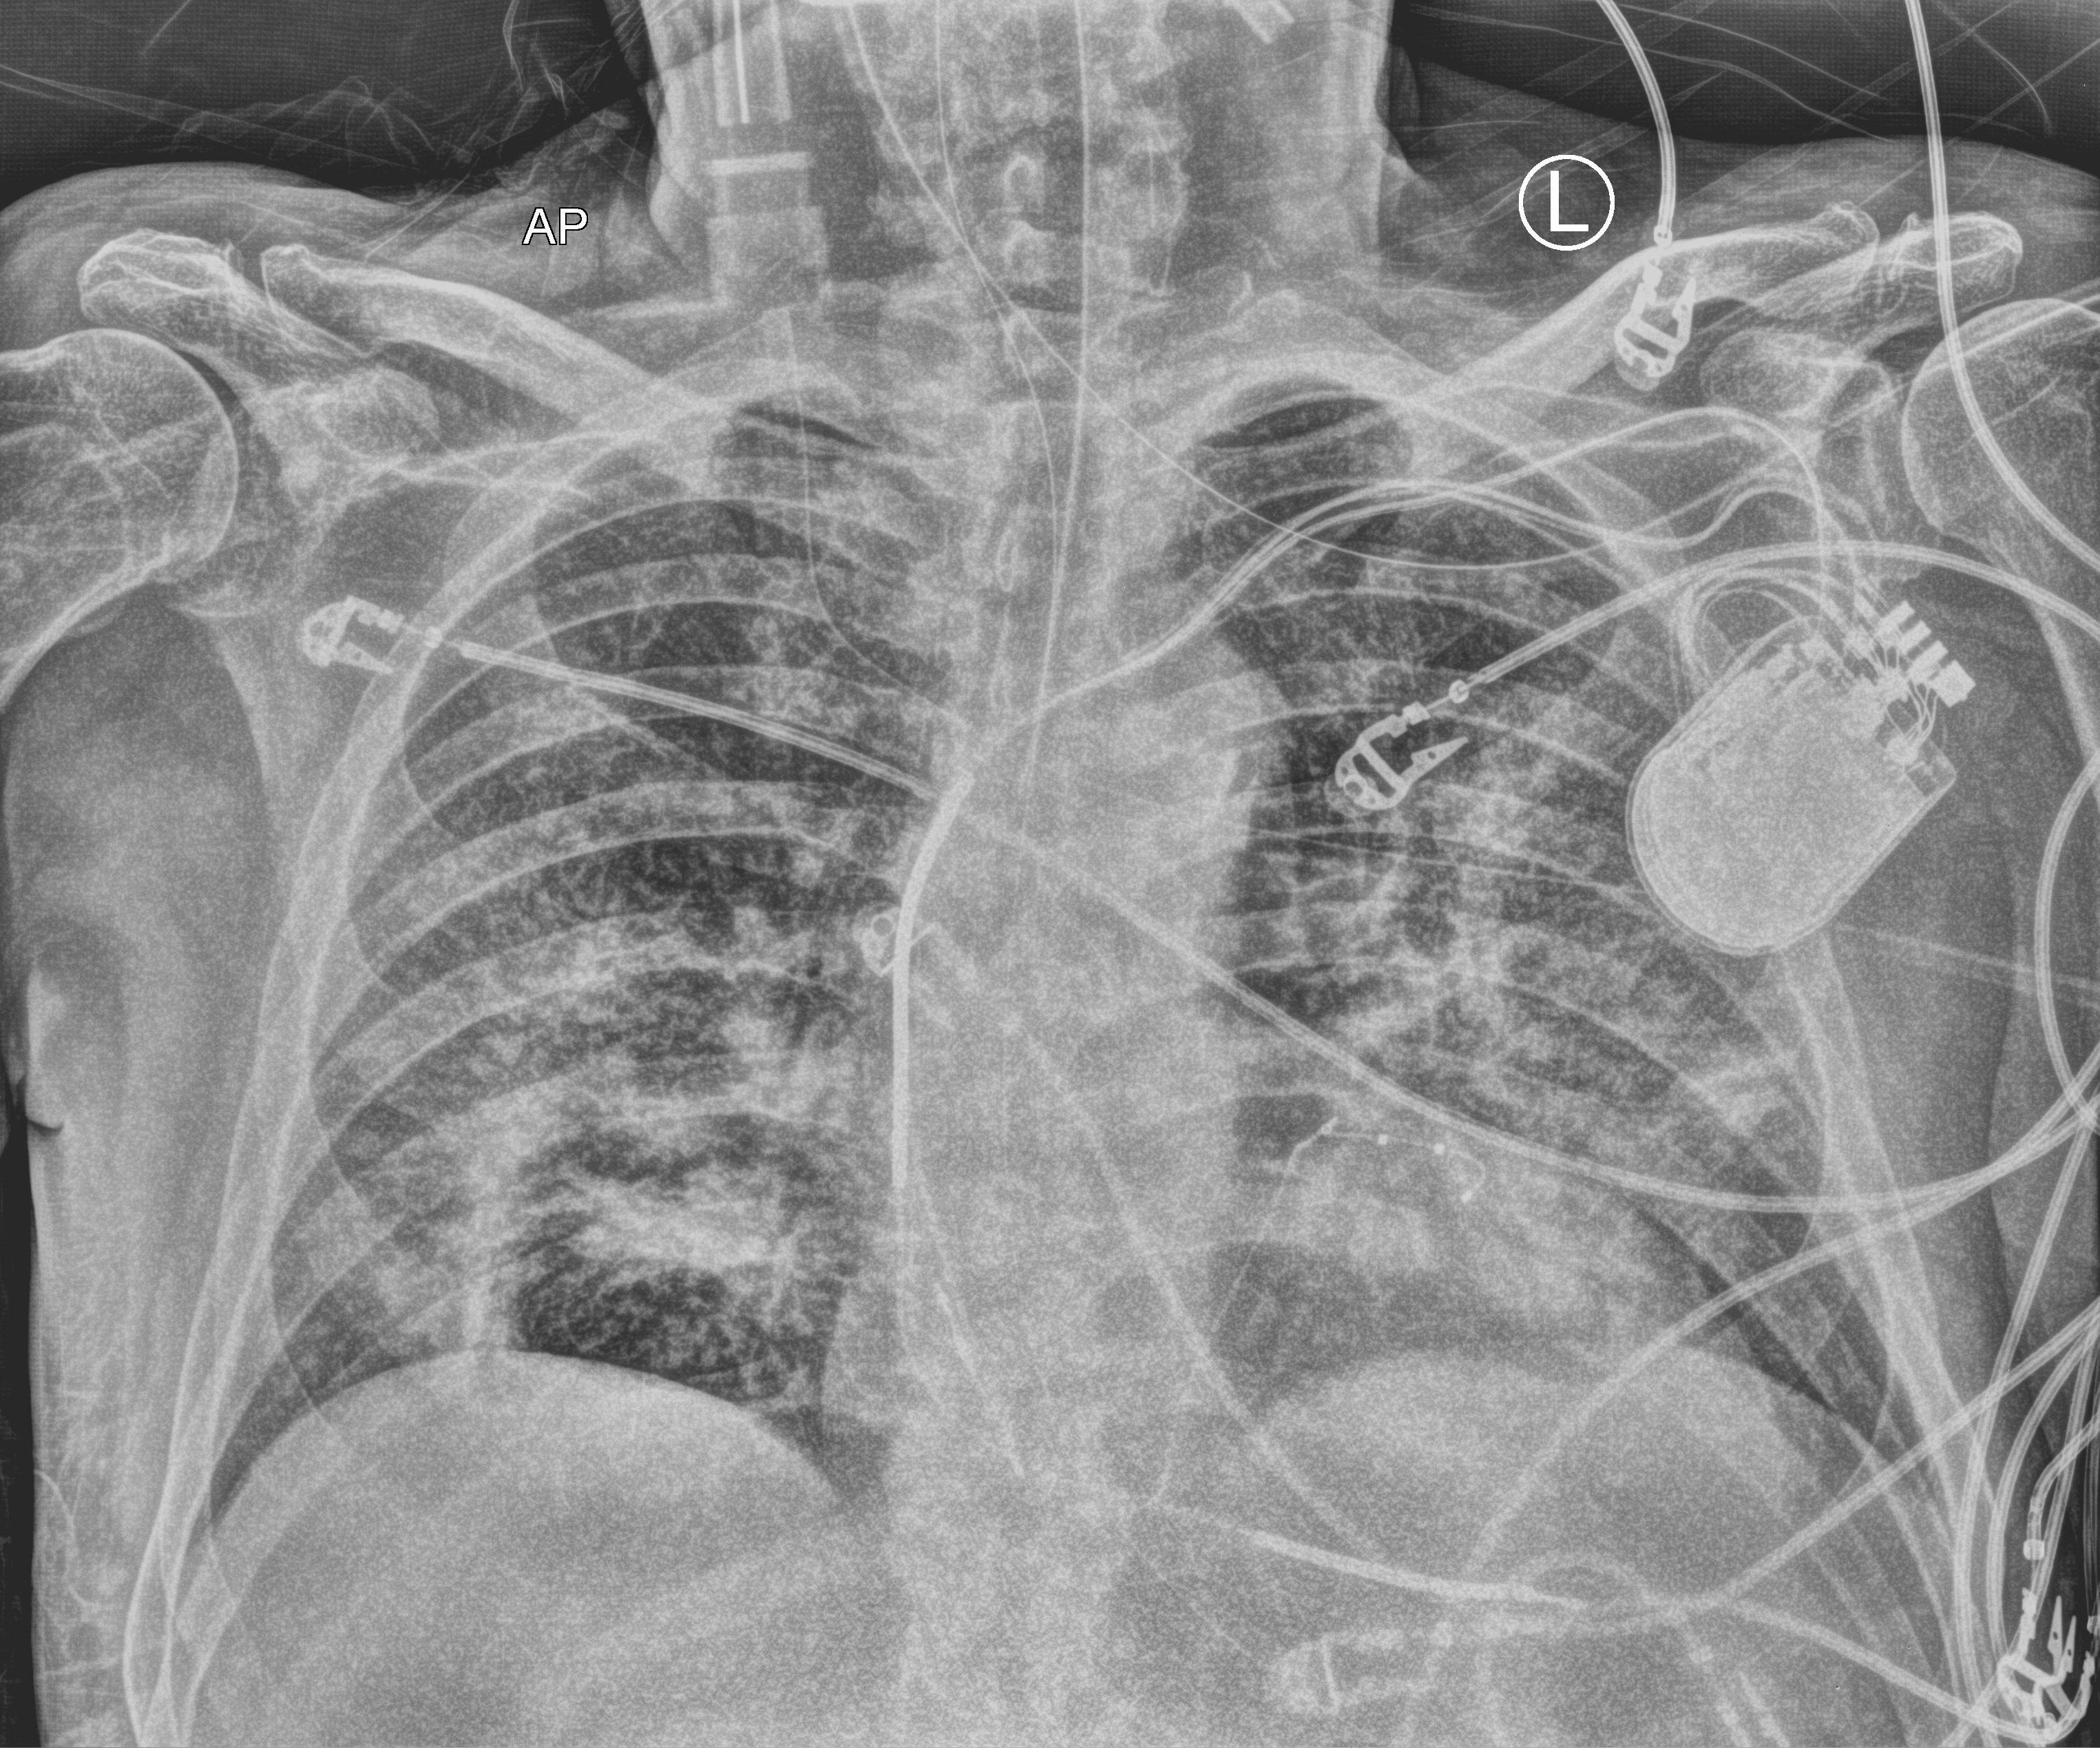
Chest X-ray (portable); anteroposterior (AP) projection. Patient hospitalised with COVID-19; male, aged 60–74 years.
Admission-level facts for this patient (not findings on this image; timing relative to this image not recorded):
- chronic kidney disease (admission record): no